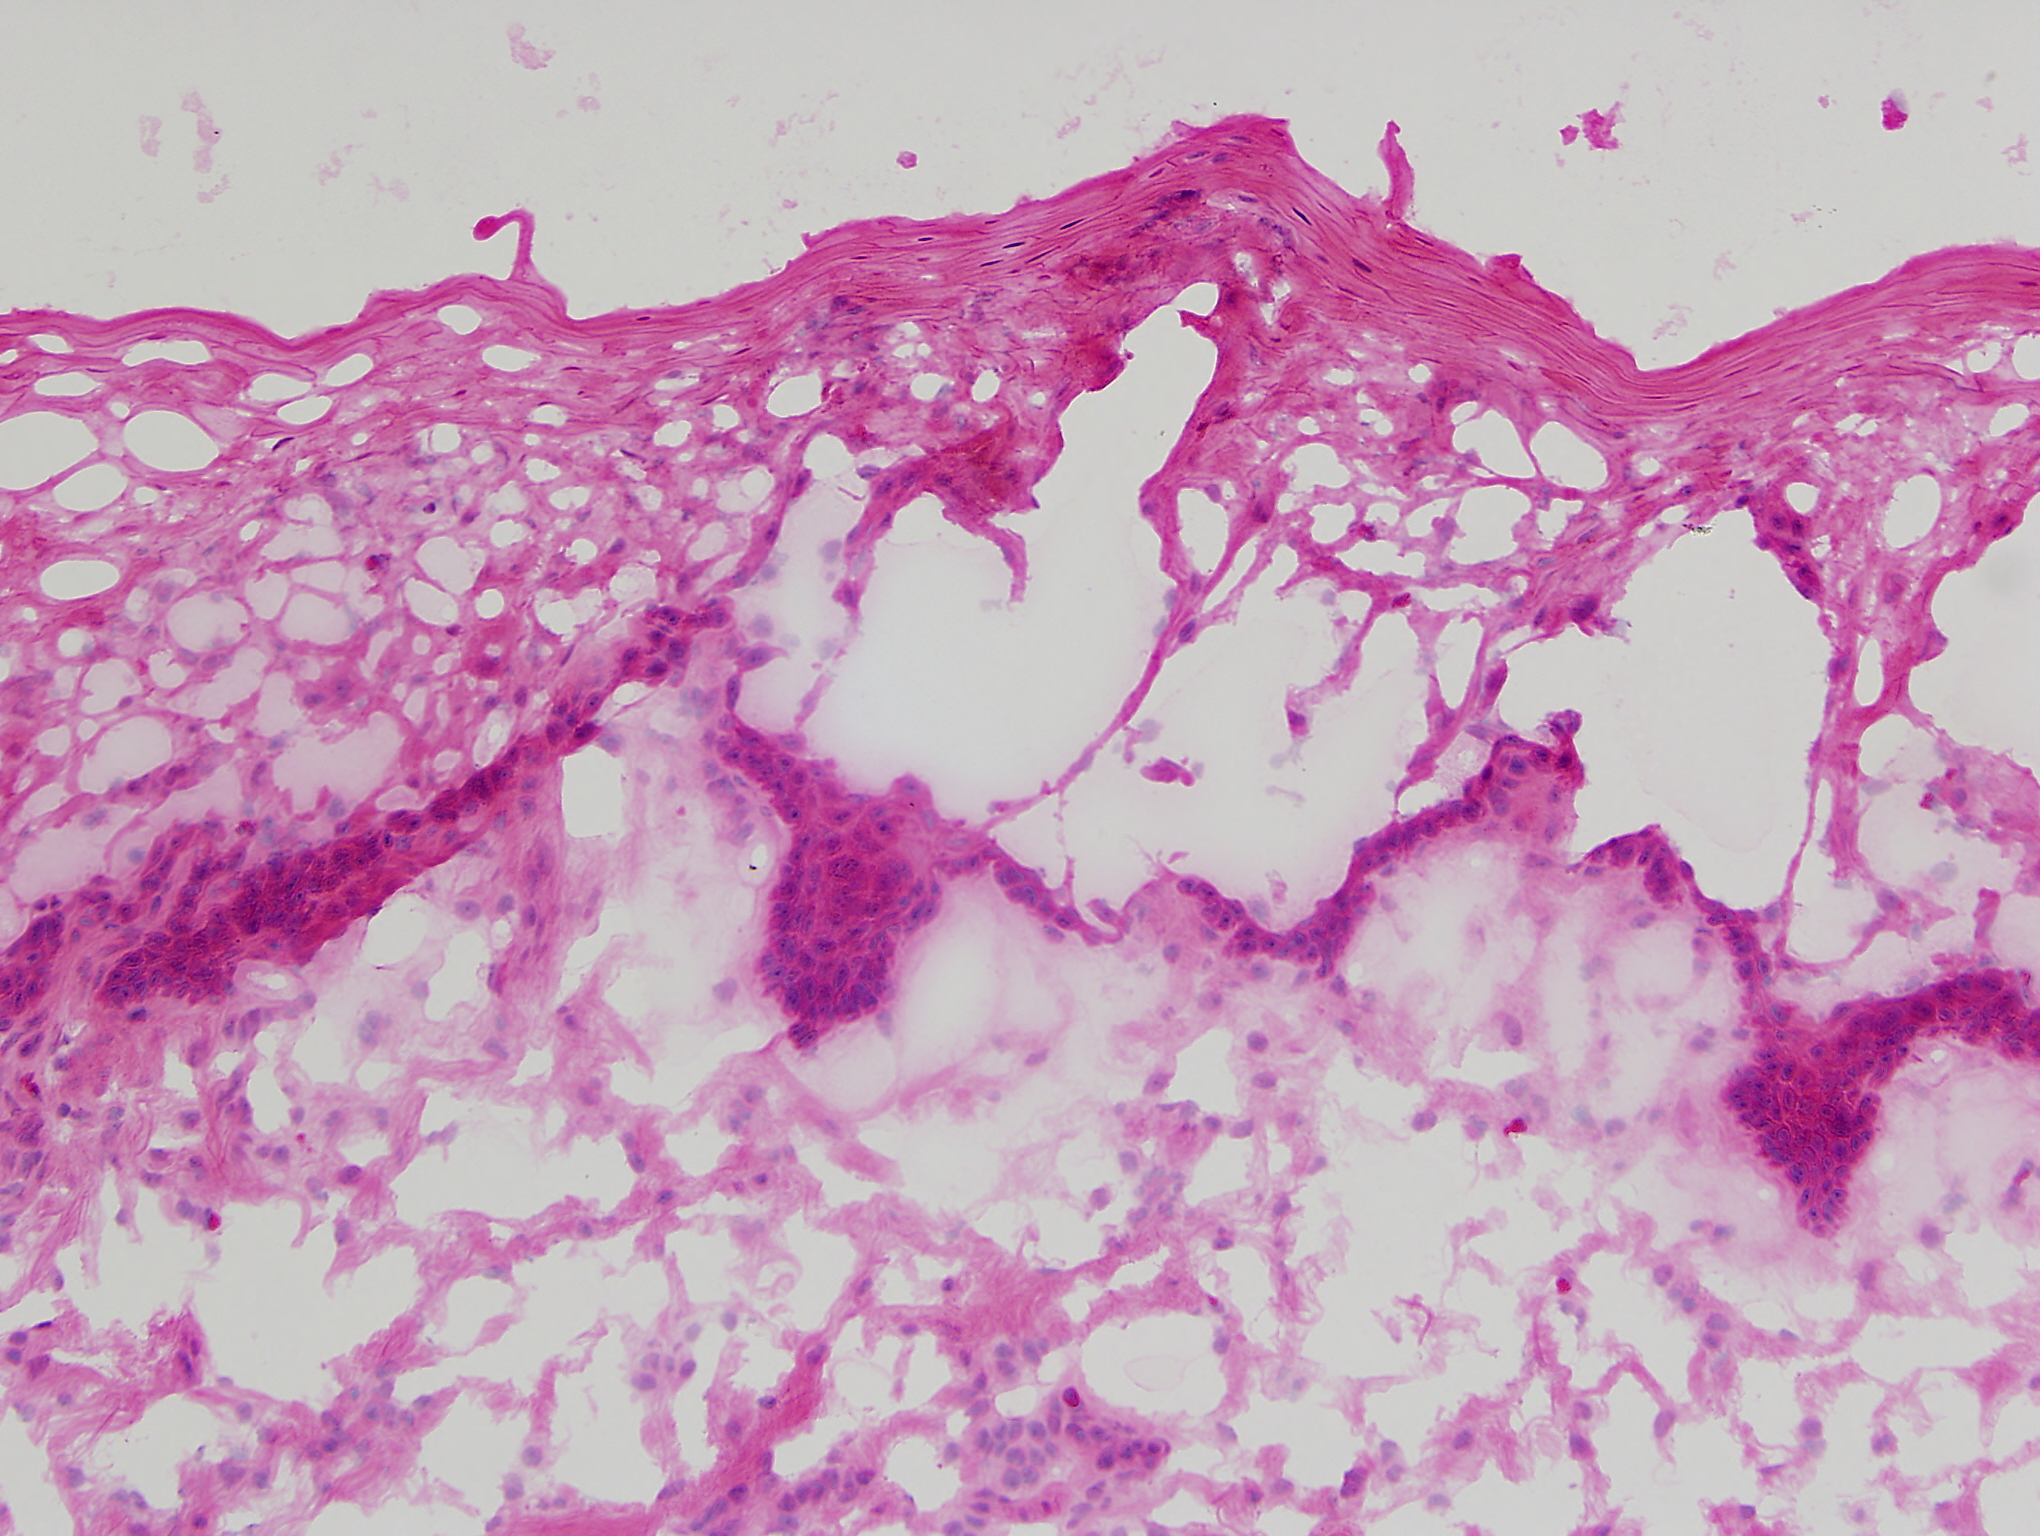
H&E image of one small field of the section, roughly 1.0 x 0.8 mm in extent; frozen section from the top of the tissue portion; solid tissue normal (non-tumour tissue) sample from the head and neck. Patient: female, age at initial diagnosis 57 years. Inflammatory infiltration, as recorded: lymphocyte infiltration 1%.
This section: solid tissue normal (non-tumour) sample from the same patient. Patient diagnosis: Squamous cell carcinoma, NOS (overlapping lesion of lip, oral cavity and pharynx).